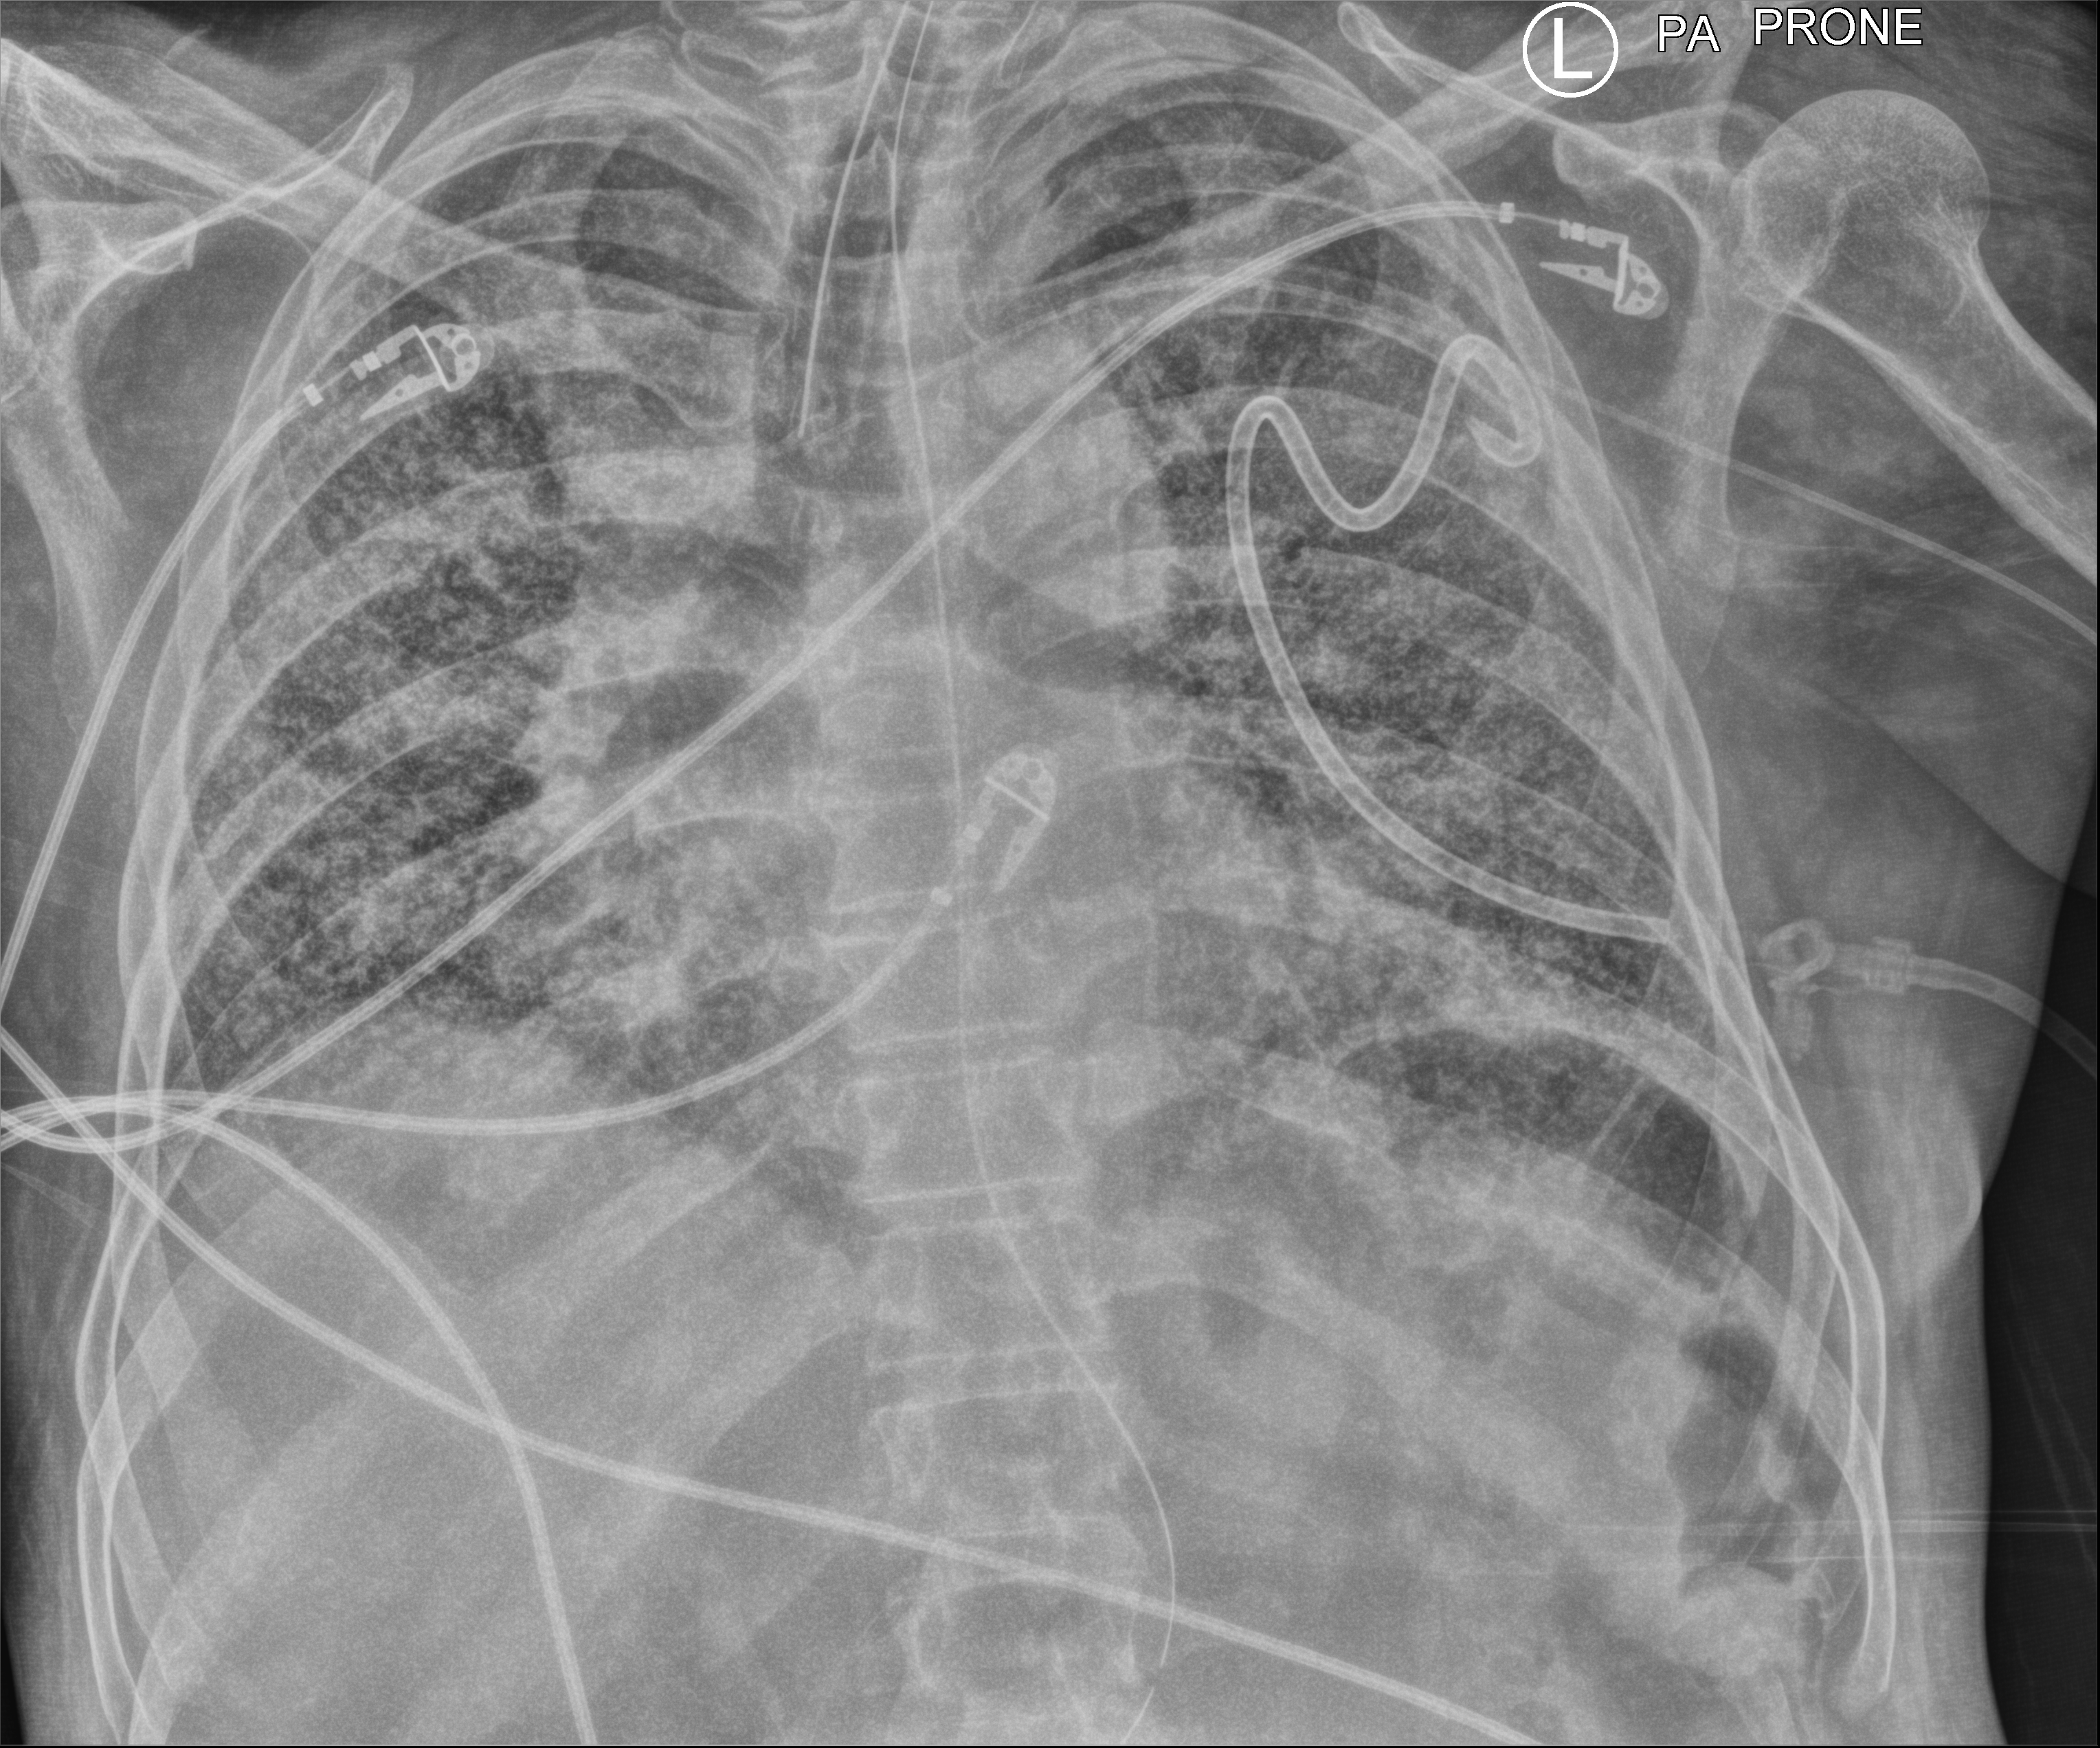
Bedside chest radiograph (computed radiography), posteroanterior (PA) projection. Patient hospitalised with COVID-19; male, aged 60–74 years.
From the hospital-stay record, not from the radiograph (when in the stay this image was taken is not recorded): mechanically ventilated during this hospital stay: yes; admitted to intensive care during this hospital stay: yes.